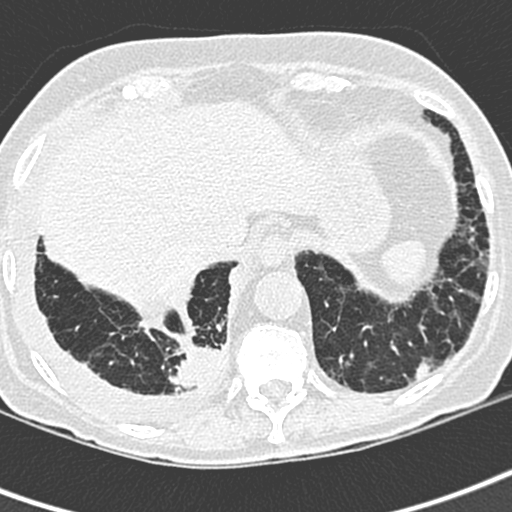
Low-dose screening chest CT, one axial slice; 120 kVp; lung window (W 1500 / L -600 HU); 1.3 mm slice thickness; 512 × 512 image matrix, field of view 288 × 288 mm.
Outlined on this slice (manually delineated by an expert):
- lesion 1 (tumor, lower lobe of right lung): bounding box (x1, y1, x2, y2) in pixels: (169, 344, 220, 390)
- lesion 2 (nodule, lower lobe of left lung): (415, 363, 431, 377)